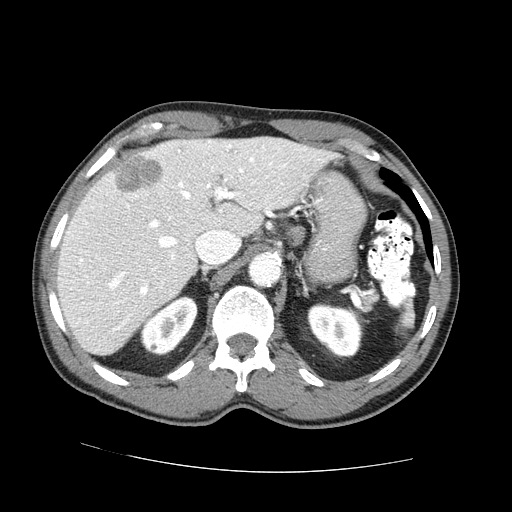
Contrast-enhanced abdominal CT (liver protocol), one axial slice. Position 49 of 73 along the scan axis. Reconstruction kernel STANDARD. 100 kVp. One of 2 acquisitions stored at this slice position. Soft-tissue window (W 400 / L 40 HU). 512 × 512 image matrix, field of view 380 × 380 mm. From the clinical record (not read from this slice): diagnosis: hepatocellular carcinoma (patient treated with transarterial chemoembolisation; whether this scan precedes or follows treatment is not stated here); TNM stage (as recorded): Stage-IVA; Child-Pugh class: A; tumour differentiation: no biopsy; tumour nodularity: uninodular.
Structures marked on this image (semi-automatically segmented with operator editing):
- liver parenchyma outside the tumour (the mass and vessels are separate outlines, so this box may not span the whole liver): bounding box [x1, y1, x2, y2] px = [56, 136, 334, 354]
- mass: [114, 155, 161, 192]
- liver vessels: [80, 141, 286, 331]